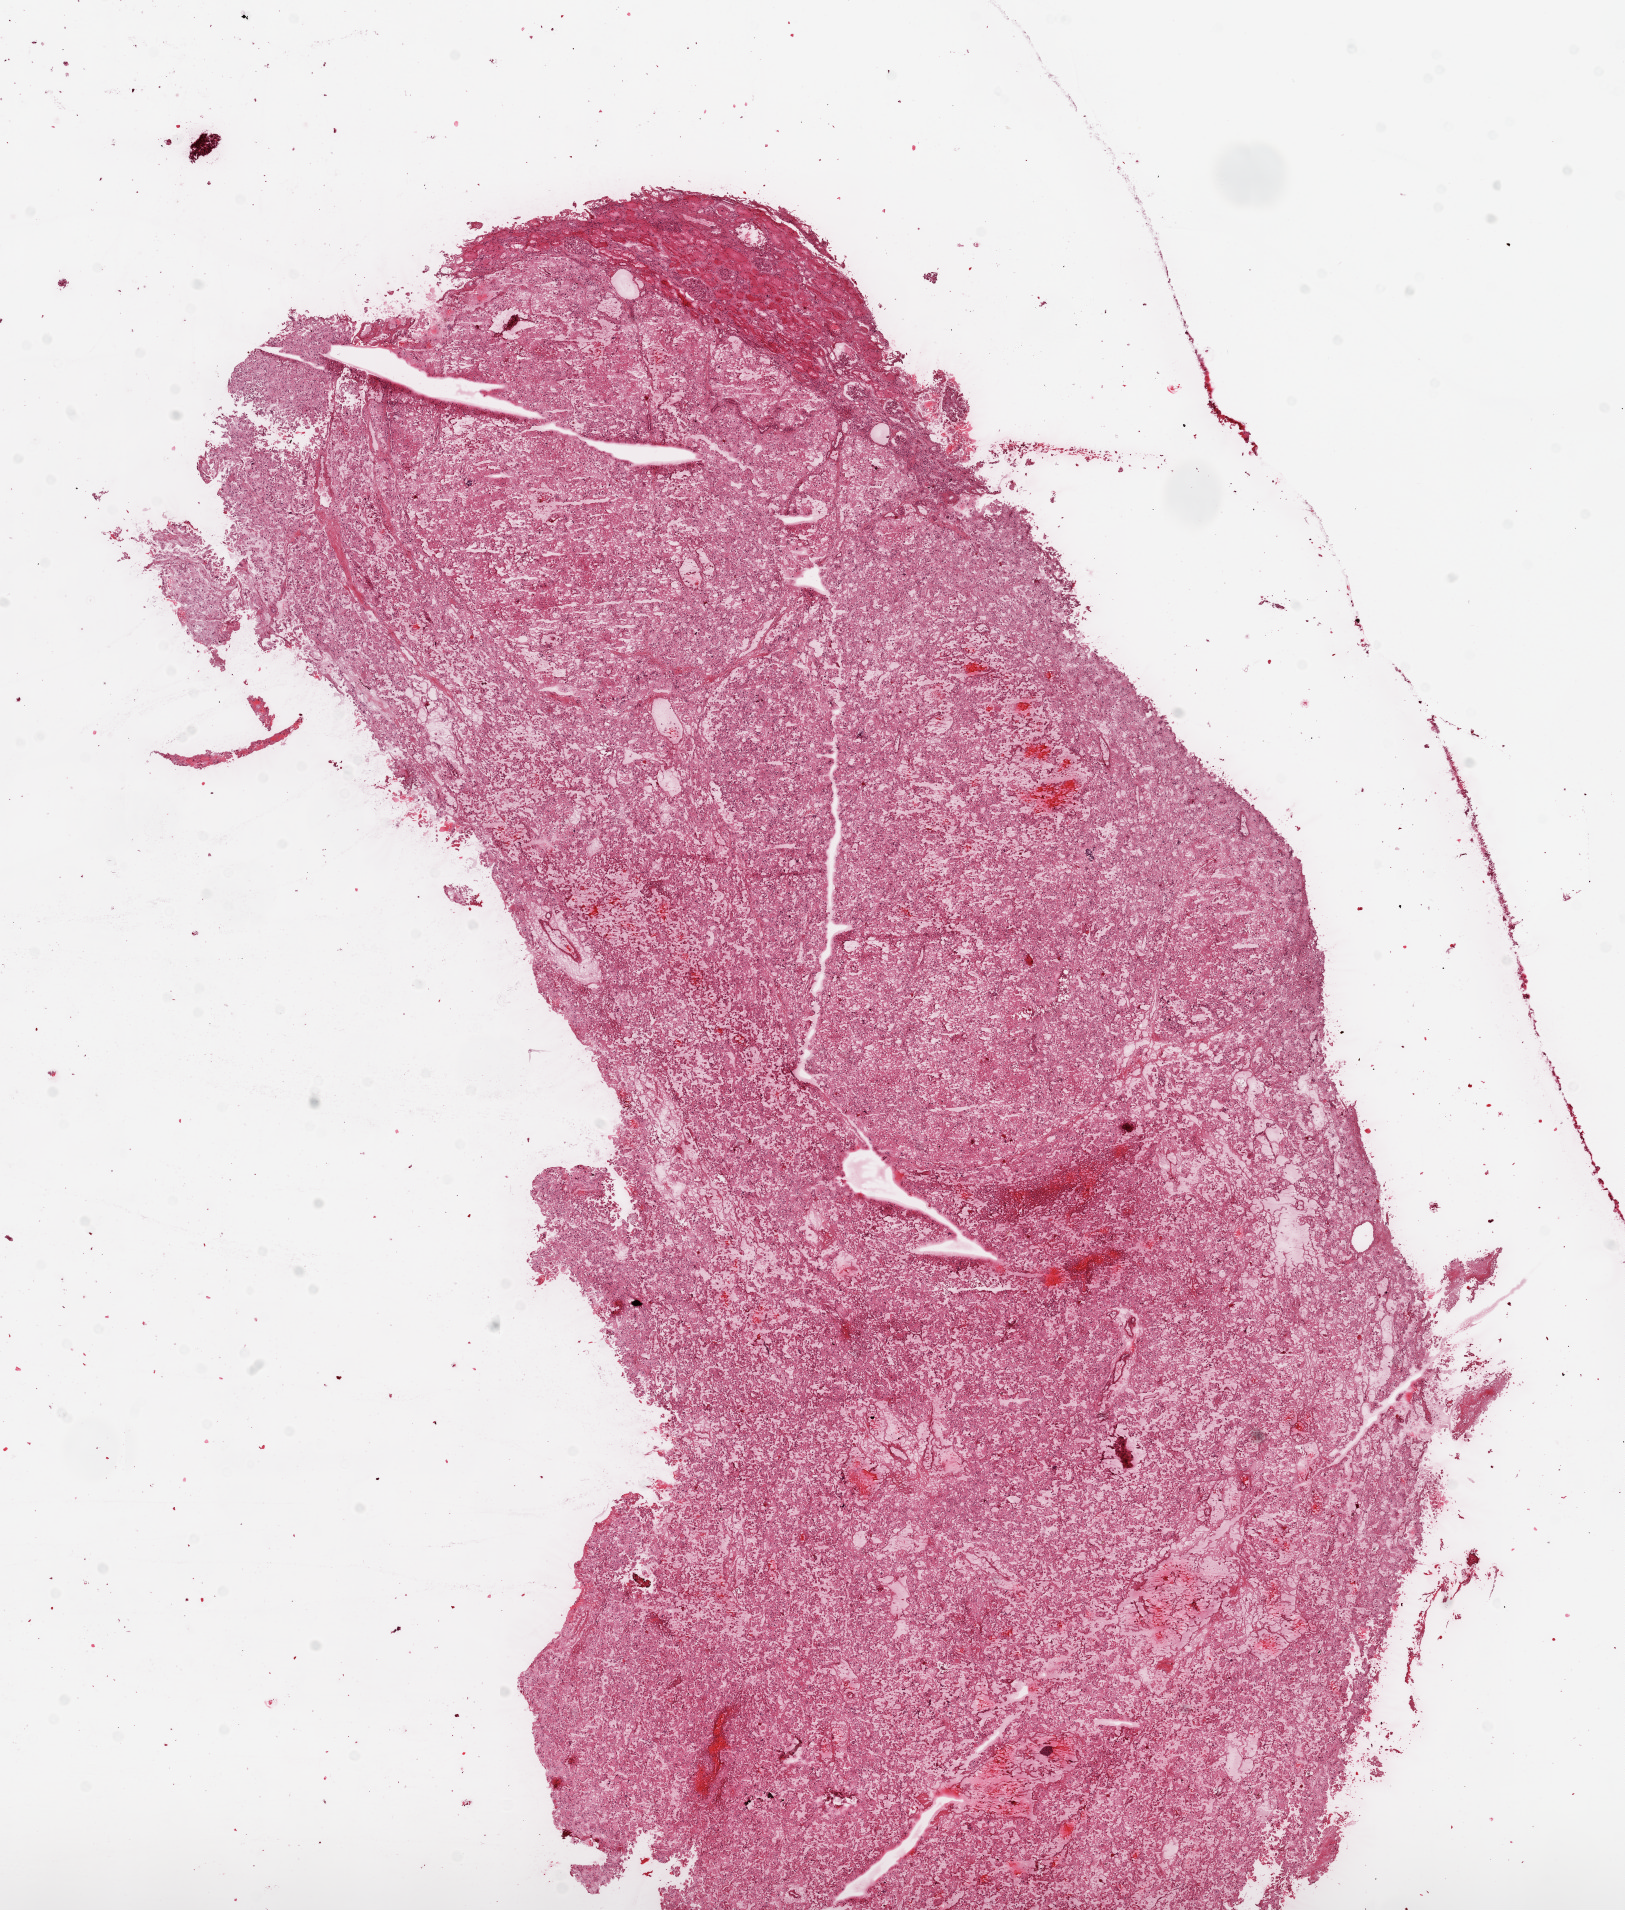
Whole-slide histology image, H&E, low-resolution overview of the scanned area, about 13.0 x 15.3 mm. Frozen section from the top of the tissue portion. Kidney, primary tumour sample. Male, age 54 years at initial diagnosis. Histologic grade: G3 (poorly differentiated). Pathologist review of this section (percent, as recorded): tumour cells 85%, tumour nuclei 85%, normal cells 5%, stromal cells 10%, necrosis 0%.
Histologic diagnosis: Clear cell adenocarcinoma, NOS. AJCC pathologic stage: I. Laterality: left.